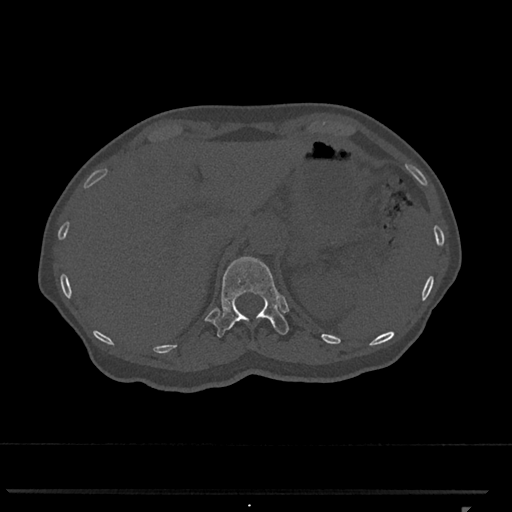
CT including the spine, one axial slice; position 469 of 793 along the scan axis; bone window (W 1800 / L 400 HU); 0.5 mm slice thickness; 512 × 512 image matrix, field of view 380 × 380 mm. Patient: female, 62 years. From the clinical record (not read from this slice): primary cancer: renal.
Annotated regions visible in this slice (semi-automatic segmentation, software-assisted and operator-edited):
- T12 vertebra: box from (x=213, y=256) to (x=289, y=338) px